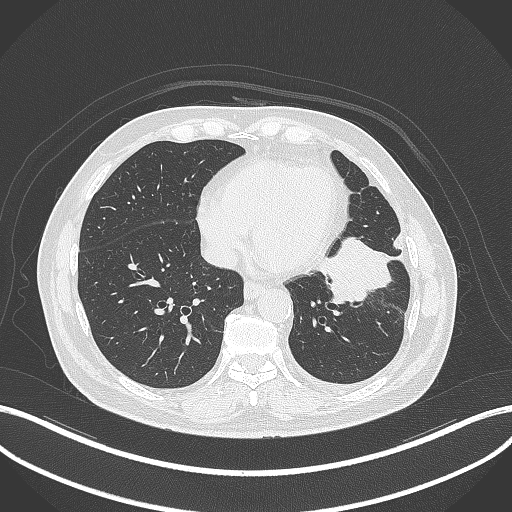
Chest CT, one axial slice. Position 119 of 230 along the scan axis. Reconstruction kernel B70f. 120 kVp. Lung window (W 1500 / L -600 HU). 1 mm slice thickness. 512 × 512 image matrix, field of view 400 × 400 mm. Male patient, age 68 years. From the clinical record (not read from this slice): clinical TNM (as recorded): T2b N0 M0.
Outlined on this slice (rectangle marked by the reading radiologist):
- lung tumour (recorded histology: squamous cell carcinoma): box from (x=319, y=233) to (x=394, y=310) px